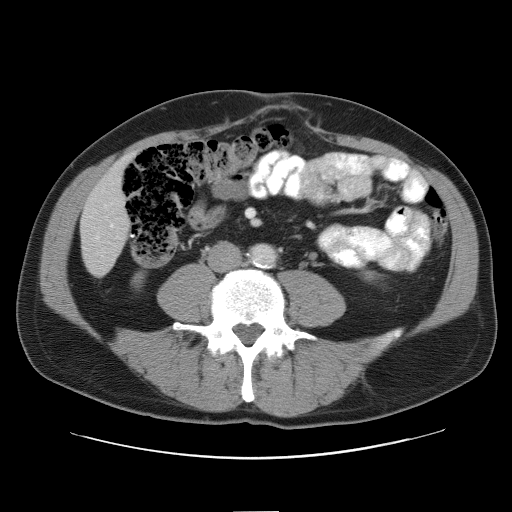
Contrast-enhanced abdominal CT, one axial slice; slice 14 of 52 in the series (ordered by position); intravenous contrast given; soft-tissue window (W 400 / L 40 HU); 5 mm slice thickness; 512 × 512 image matrix. Male patient, age 70 years. Case-level facts recorded for this patient, not image findings: diagnosis: colorectal cancer liver metastases, imaged before liver resection; multiple liver metastases: yes; largest metastasis: 4 cm; disease in both lobes: yes.
Annotated regions visible in this slice (manually delineated by an expert):
- liver: bounding box [x1, y1, x2, y2] px = [81, 162, 131, 275]
- portal vein (with intrahepatic branches): [110, 224, 114, 227]